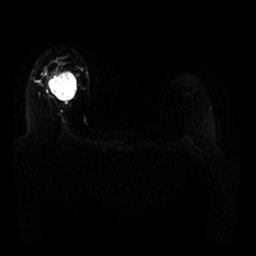
Breast MRI, one axial slice; position 19 of 25 along the scan axis; diffusion-weighted series; image 2 of 4 stored at this slice position (different b-values; order by instance number); 1.5 T; 4 mm slice thickness; 256 × 256 image matrix, field of view 330 × 330 mm. Female patient.
Structures marked on this image (outlined manually by an expert reader):
- tumour on diffusion-weighted imaging: bounding box [x1, y1, x2, y2] px = [47, 71, 64, 89]